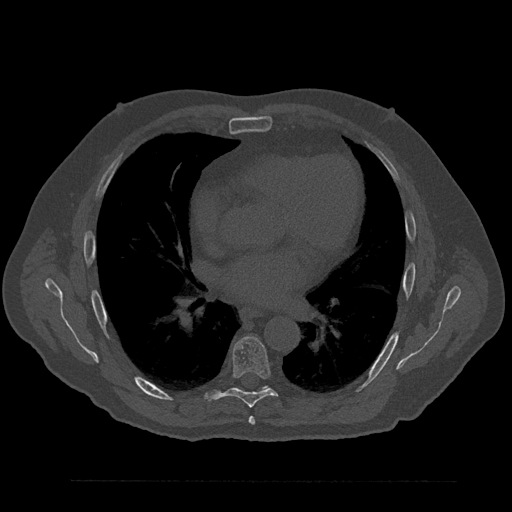
CT including the spine, one axial slice; position 503 of 797 along the scan axis; reconstruction kernel Br40s/3; bone window (W 1800 / L 400 HU); 512 × 512 image matrix, field of view 430 × 430 mm. Male patient, age 61 years. From the clinical record (not read from this slice): primary cancer: prostate.
Outlined on this slice (semi-automatically segmented with operator editing):
- T6 vertebra: box from (x=249, y=416) to (x=255, y=425) px
- T7 vertebra: (x=207, y=336)–(x=278, y=408)
- T8 vertebra: (x=264, y=386)–(x=268, y=388)